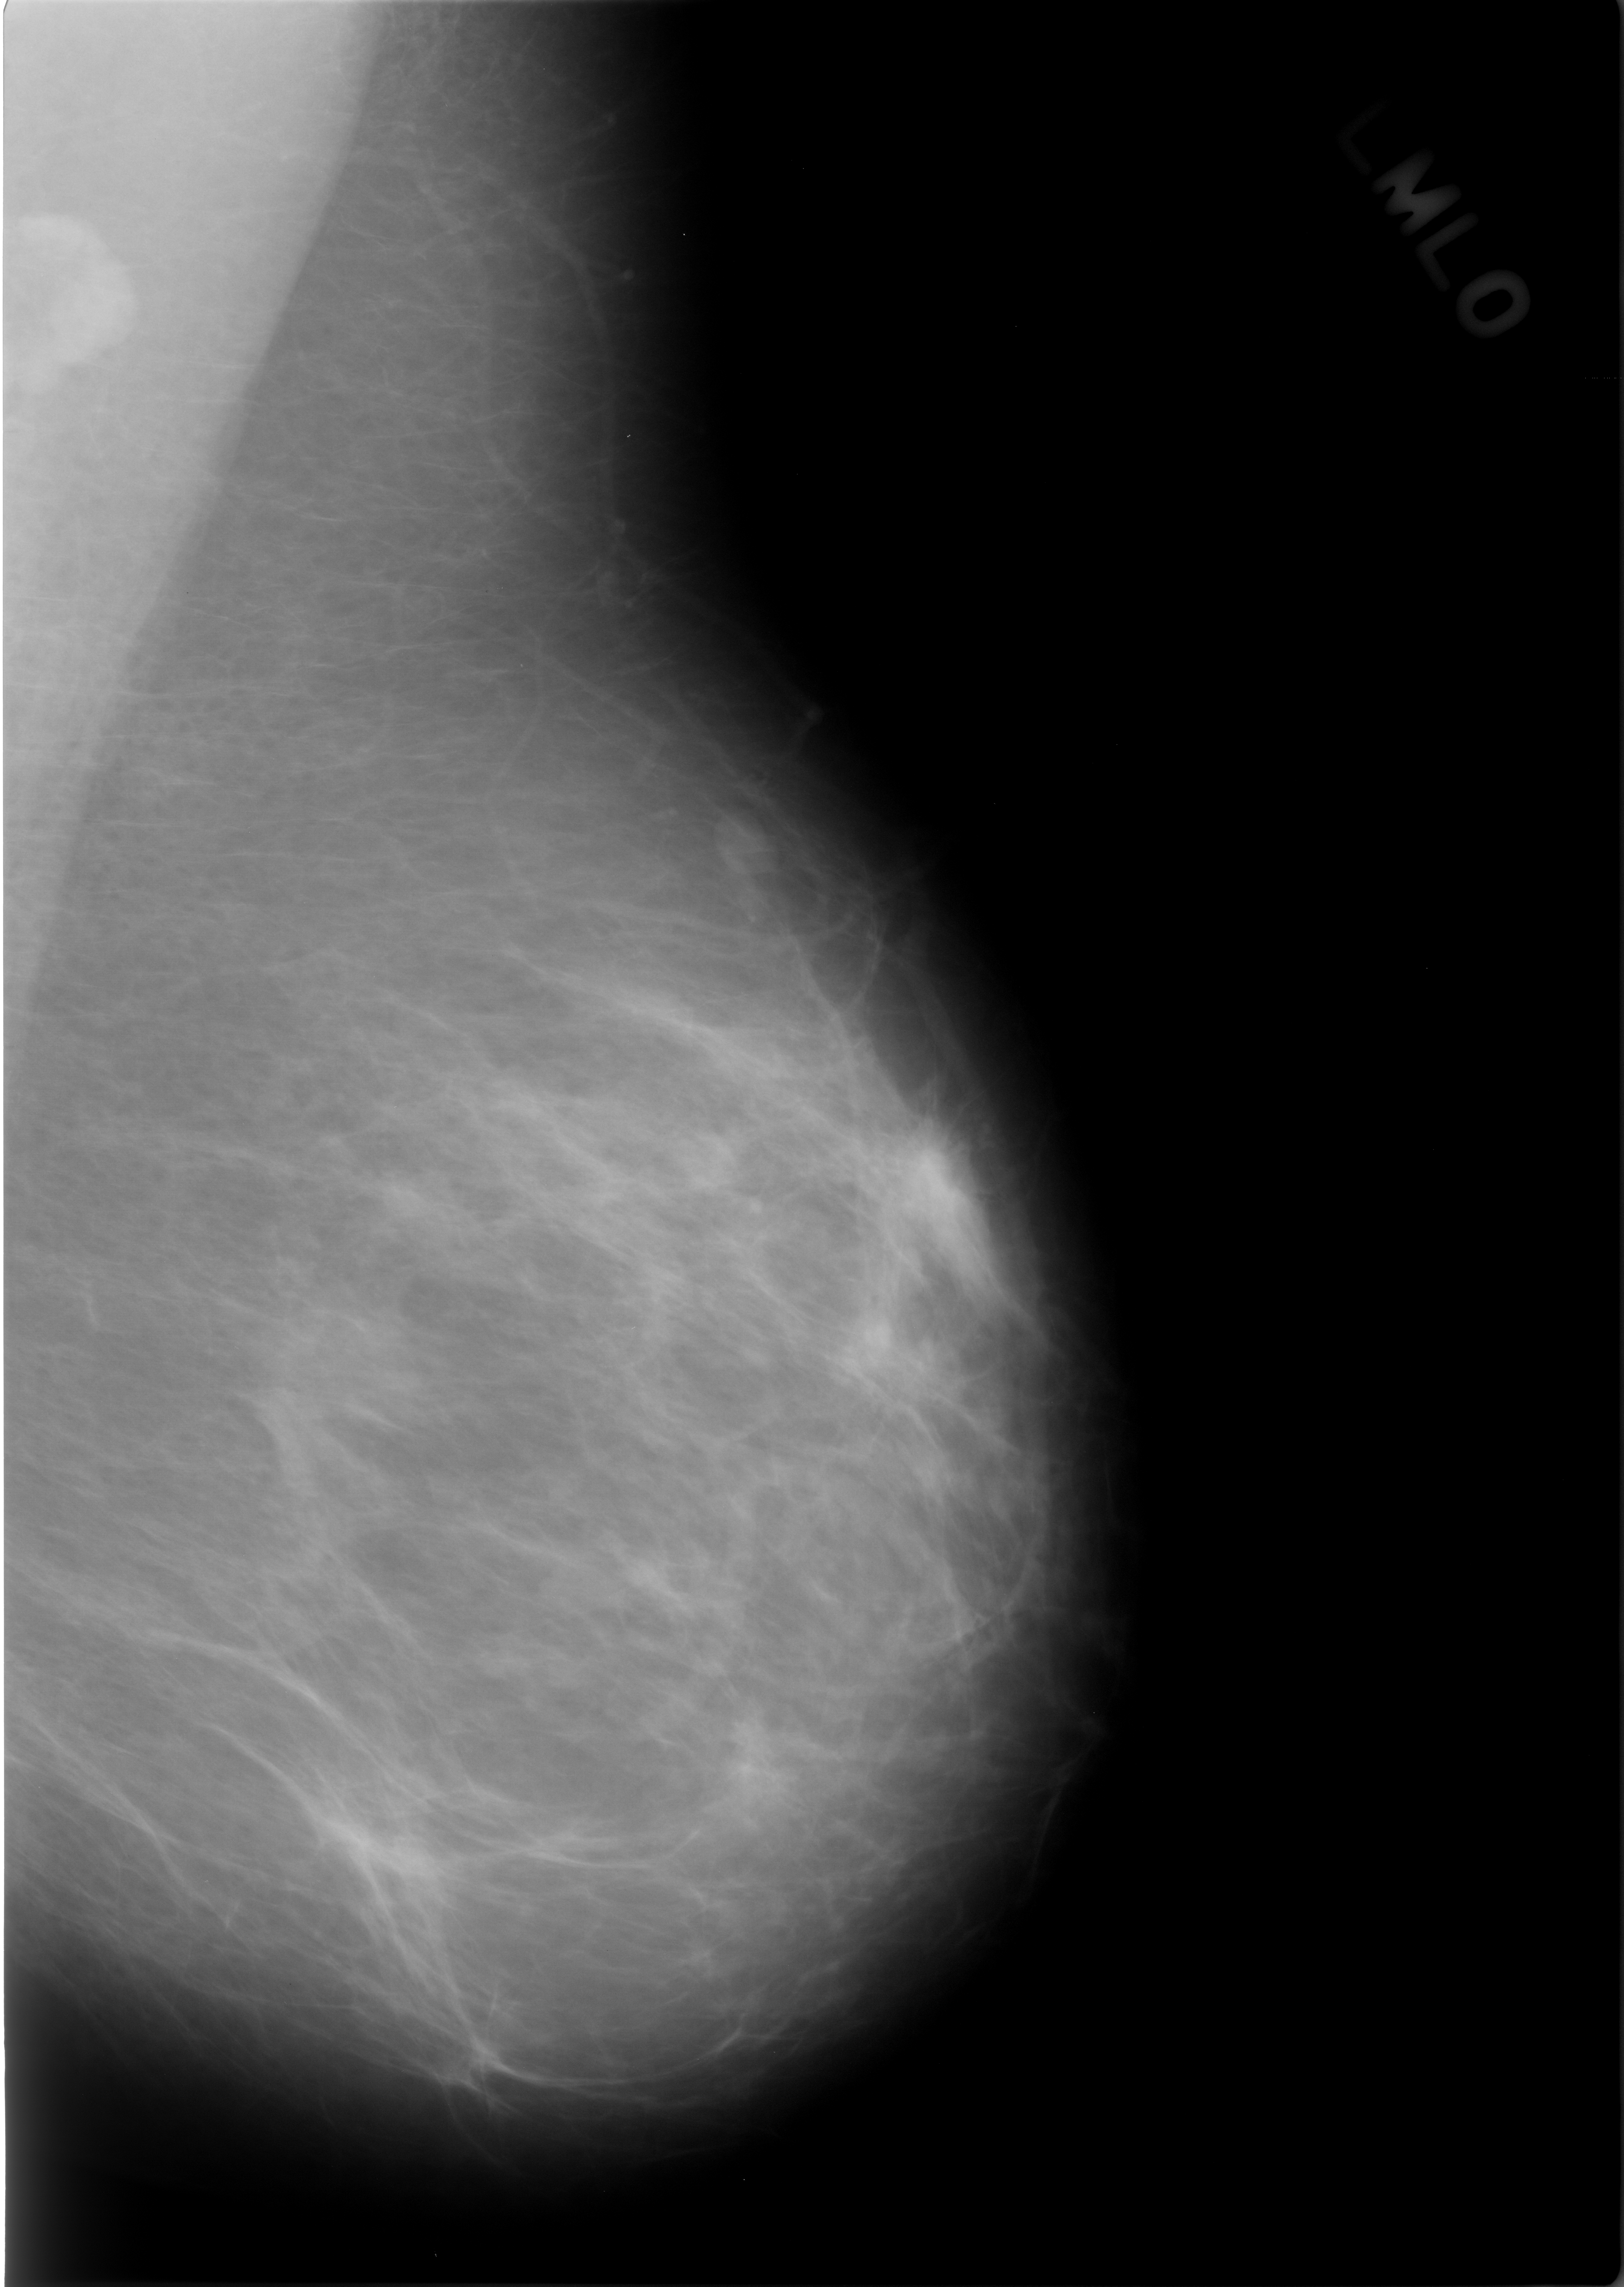
Mammogram (digitized film); left breast; MLO view; breast composition: almost entirely fatty (BI-RADS density category 1 of 4); 1624 × 2287 image matrix.
Expert-marked regions of interest on this film, with their recorded descriptors:
- mass, shape irregular, margins spiculated; BI-RADS assessment category 4; outcome (as recorded, no biopsy): benign without callback (not worked up further): bounding box (x1, y1, x2, y2) in pixels: (887, 1115, 1002, 1286)